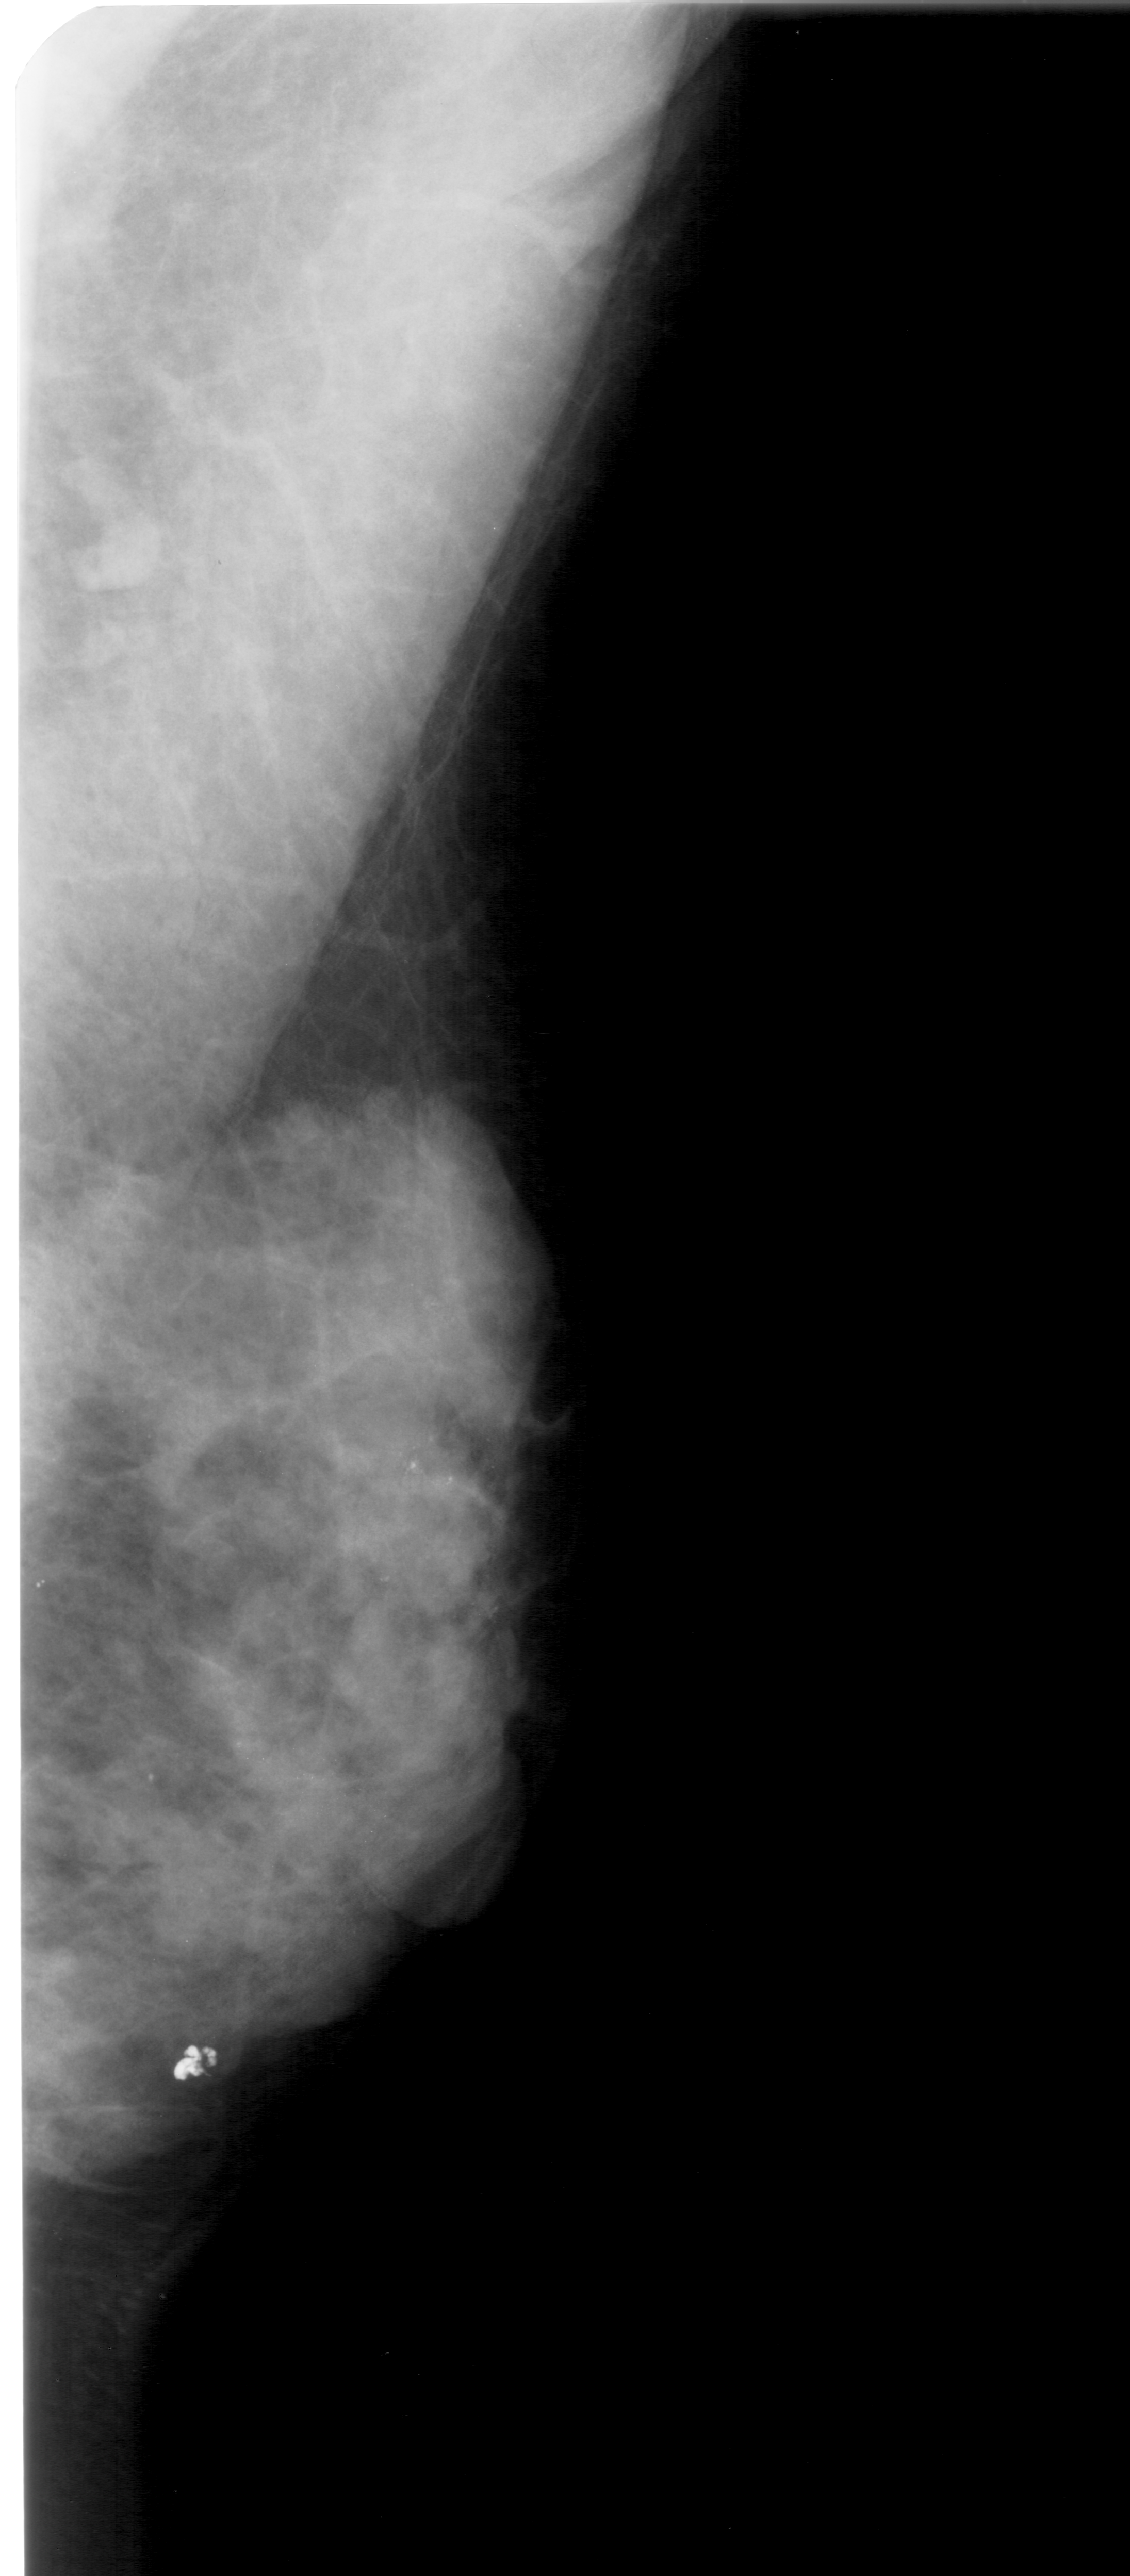
Scanned film-screen mammogram; right breast; MLO view; breast composition: extremely dense (BI-RADS density category 4 of 4).
Radiologist-marked abnormalities on this image: calcifications, morphology pleomorphic, distribution clustered; BI-RADS assessment category 4; subtlety rating 3 on a 1 (subtle) to 5 (obvious) scale; pathology (as recorded): malignant.